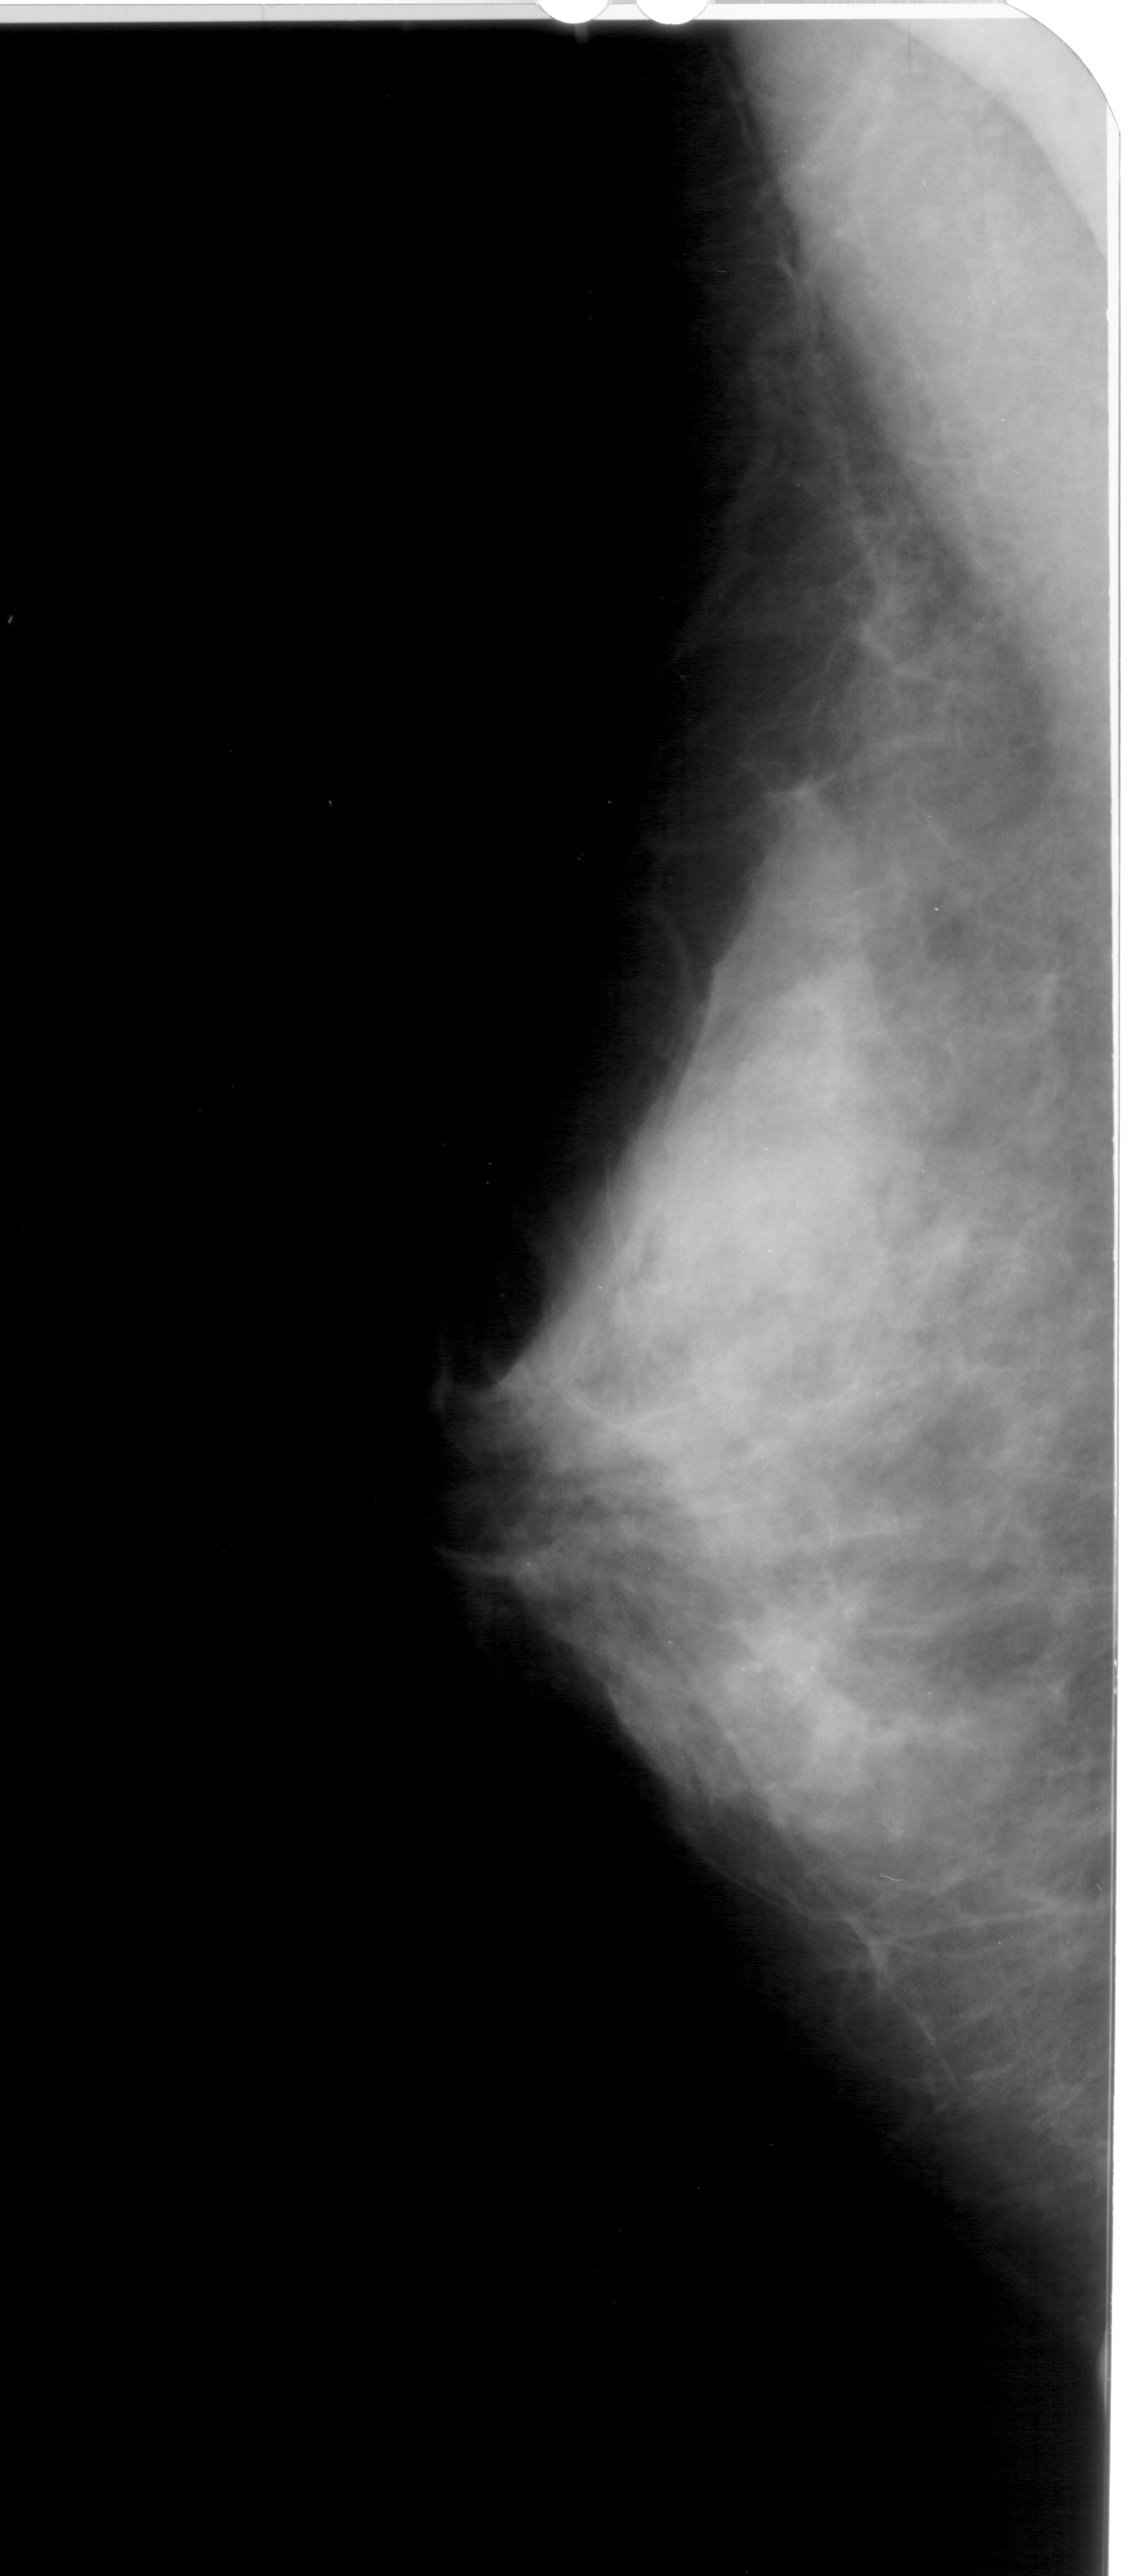
Mammogram (digitized film), left breast, MLO view, breast composition: extremely dense (BI-RADS density category 4 of 4).
Radiologist-marked abnormalities on this image: calcifications, morphology amorphous, distribution clustered; BI-RADS assessment category 4; pathology (as recorded): benign.